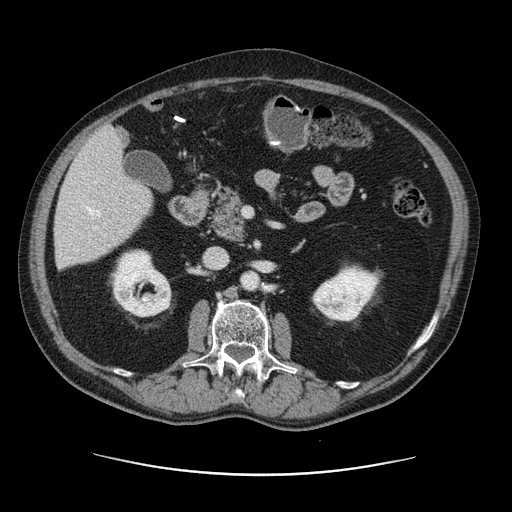
Contrast-enhanced abdominal CT, one axial slice; position 54 of 141 along the scan axis; 120 kVp; intravenous contrast given; soft-tissue window (W 400 / L 40 HU); 2.5 mm slice thickness; 512 × 512 image matrix. Male patient, age 72 years. Case-level facts recorded for this patient, not image findings: diagnosis: colorectal cancer liver metastases, imaged before liver resection; multiple liver metastases: yes; largest metastasis: 5.4 cm; disease in both lobes: yes.
Structures marked on this image (manually delineated by an expert):
- hepatic veins: box from (x=87, y=207) to (x=100, y=230) px
- liver: (x=55, y=128)–(x=152, y=268)
- planned liver remnant (the part of the liver to remain after resection): (x=55, y=177)–(x=152, y=268)